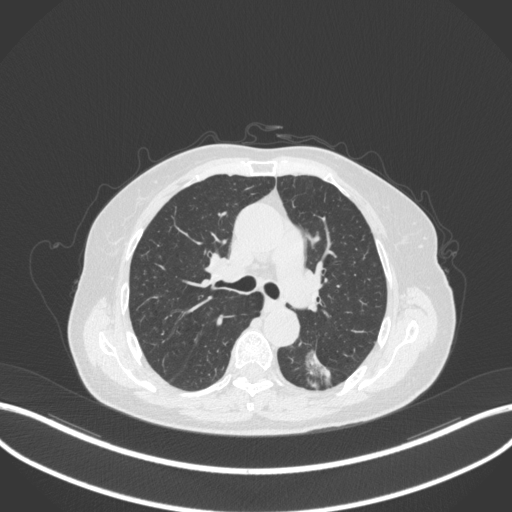
Chest CT, one axial slice. Position 192 of 352 along the scan axis. Reconstruction kernel B31f. 120 kVp. Lung window (W 1500 / L -600 HU). 512 × 512 image matrix, field of view 400 × 400 mm. Female patient, age 70 years. From the clinical record (not read from this slice): clinical TNM (as recorded): T1c N0 M0.
Structures marked on this image (bounding box drawn by a radiologist):
- lung tumour (recorded histology: adenocarcinoma): bounding box [x1, y1, x2, y2] px = [298, 346, 333, 389]